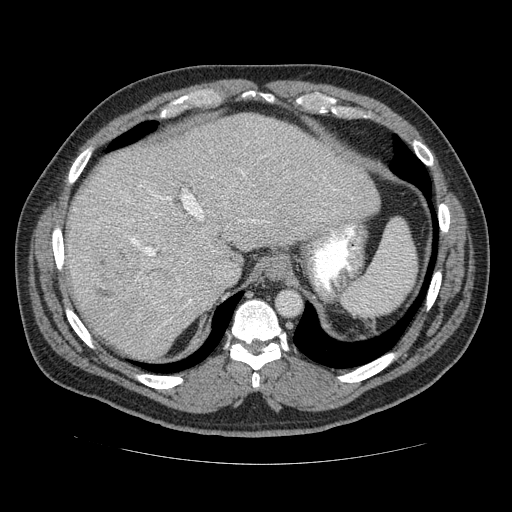
Contrast-enhanced abdominal CT (liver protocol), one axial slice; position 96 of 113 along the scan axis; soft-tissue window (W 400 / L 40 HU); 2.5 mm slice thickness; 512 × 512 image matrix, field of view 400 × 400 mm. From the clinical record (not read from this slice): diagnosis: hepatocellular carcinoma (patient treated with transarterial chemoembolisation; whether this scan precedes or follows treatment is not stated here); TNM stage (as recorded): Stage-II.
Outlined on this slice (semi-automatically segmented with operator editing):
- abdominal aorta: bounding box (x1, y1, x2, y2) in pixels: (278, 291, 301, 315)
- liver parenchyma outside the tumour (the mass and vessels are separate outlines, so this box may not span the whole liver): (62, 114, 382, 356)
- mass: (79, 214, 181, 310)
- liver vessels: (62, 176, 337, 317)